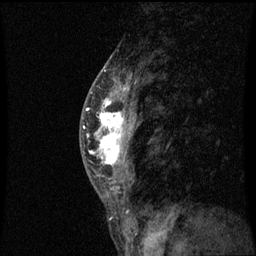
Breast MRI (dynamic contrast-enhanced), one sagittal slice. Dynamic contrast-enhanced series, image 2 of 3 at this slice position (ordered by acquisition). 1.5 T. TE 4.2 ms, TR 8.9 ms. 256 × 256 image matrix, field of view 200 × 200 mm. Patient: female, 50 years. From the clinical record (not read from this slice): setting: breast cancer imaged before/during neoadjuvant chemotherapy; receptor status: triple-negative.
Structures marked on this image (semi-automatically segmented with operator editing):
- analysis volume of interest (the breast-tissue region the enhancement analysis was run in; not a lesion): bounding box <84,80,141,171> (left, top, right, bottom; pixels)
- tumour enhancement mask (voxels above the 70 % enhancement threshold inside the analysis volume of interest): <84,88,129,165>